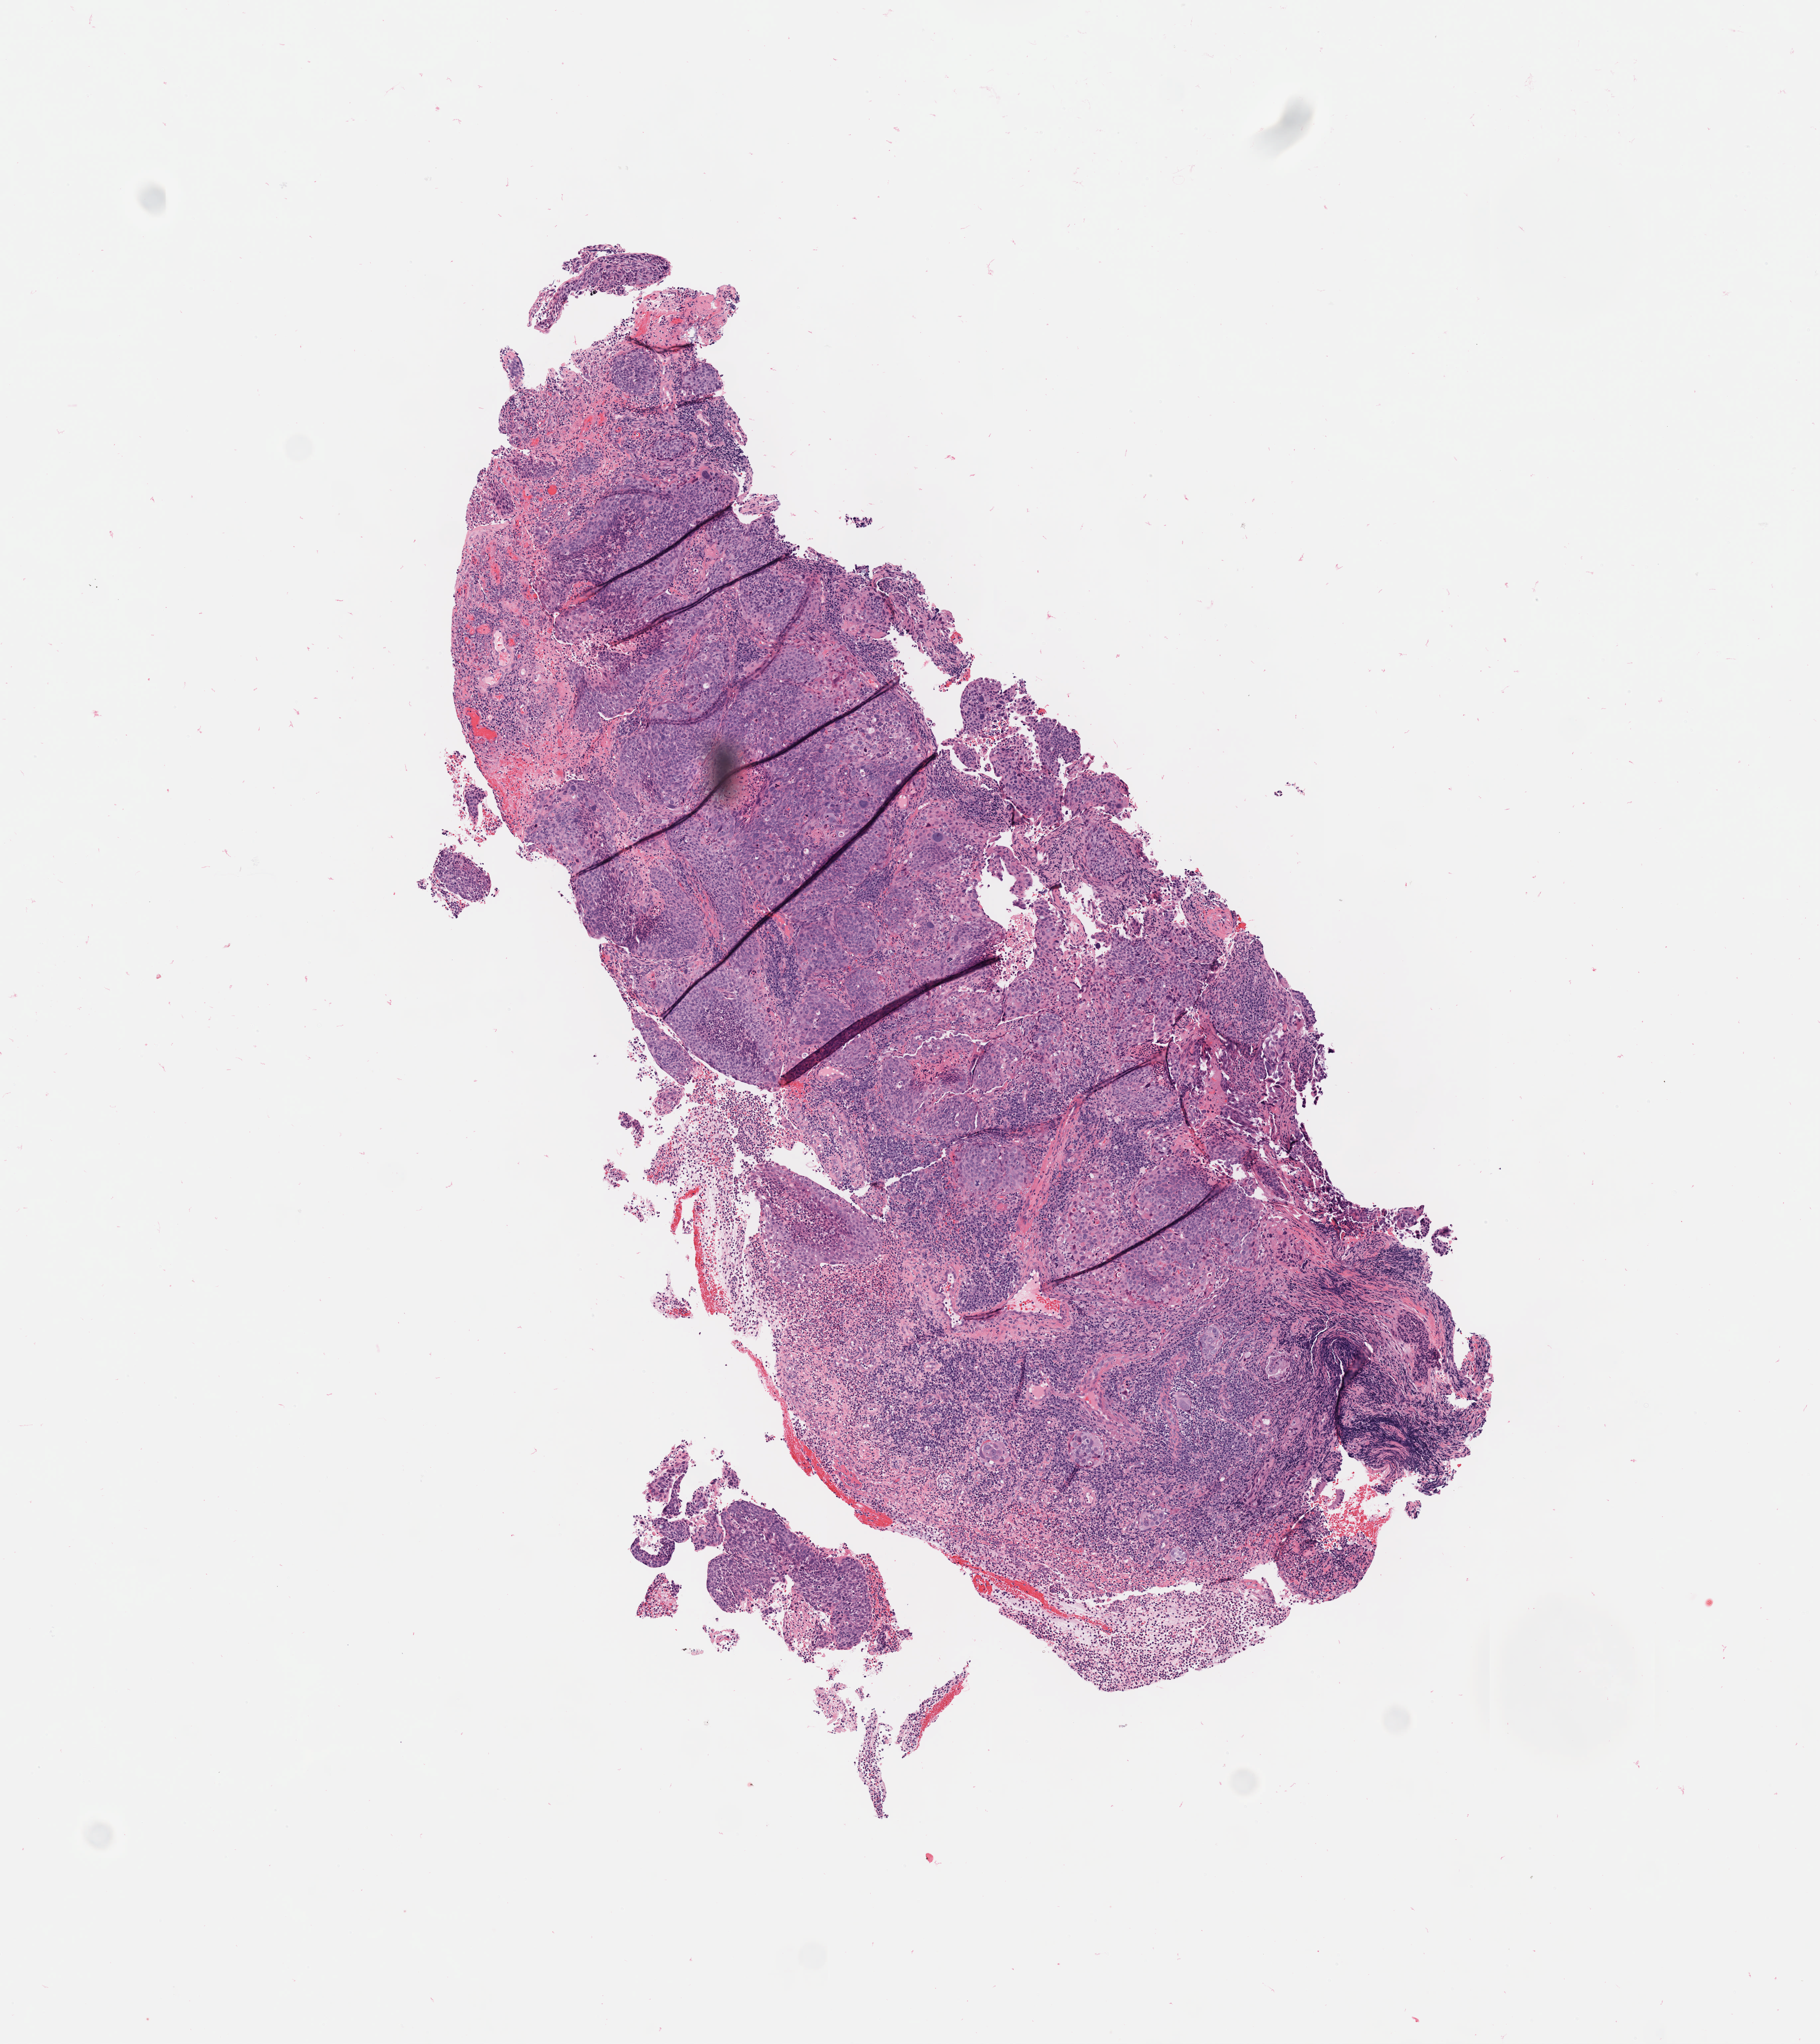
Digitized hematoxylin and eosin (H&E)-stained section — shown as a low-resolution overview of the whole scanned area (about 5.5 x 6.2 mm). Tumor tissue. Site: cervix. Female patient, 42 years old.
Histologic diagnosis: Squamous cell carcinoma, large cell, nonkeratinizing, NOS.